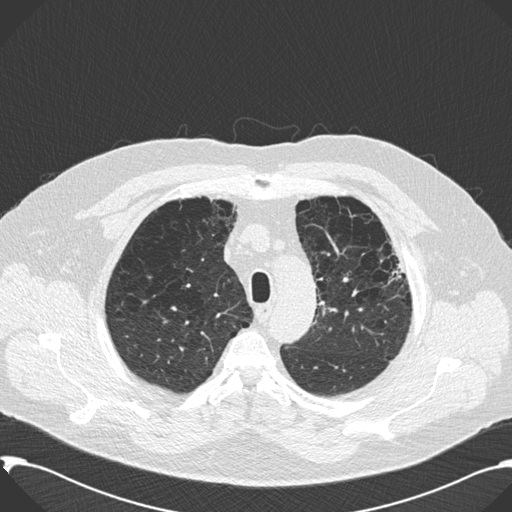
Chest CT (low-dose screening protocol), one axial image, second screening round (one year after baseline), lung window (W 1500 / L -600 HU), 2 mm slice thickness, standard (soft-tissue) reconstruction kernel (B30f), slice 36 of 199 in the series. Male participant, aged 59 years at enrolment. Current smoker at enrolment.
Expert reader's lesion annotation, bounding box [x1, y1, x2, y2] px = [365, 234, 413, 302]. No non-calcified nodule or mass ≥4 mm was recorded by the screening reader at this exam. Later outcome: lung cancer diagnosed 518 days after this screen — bronchiolo-alveolar carcinoma, mixed mucinous and non-mucinous, left upper lobe, stage IA (AJCC 6th edition), 20 mm at pathology.